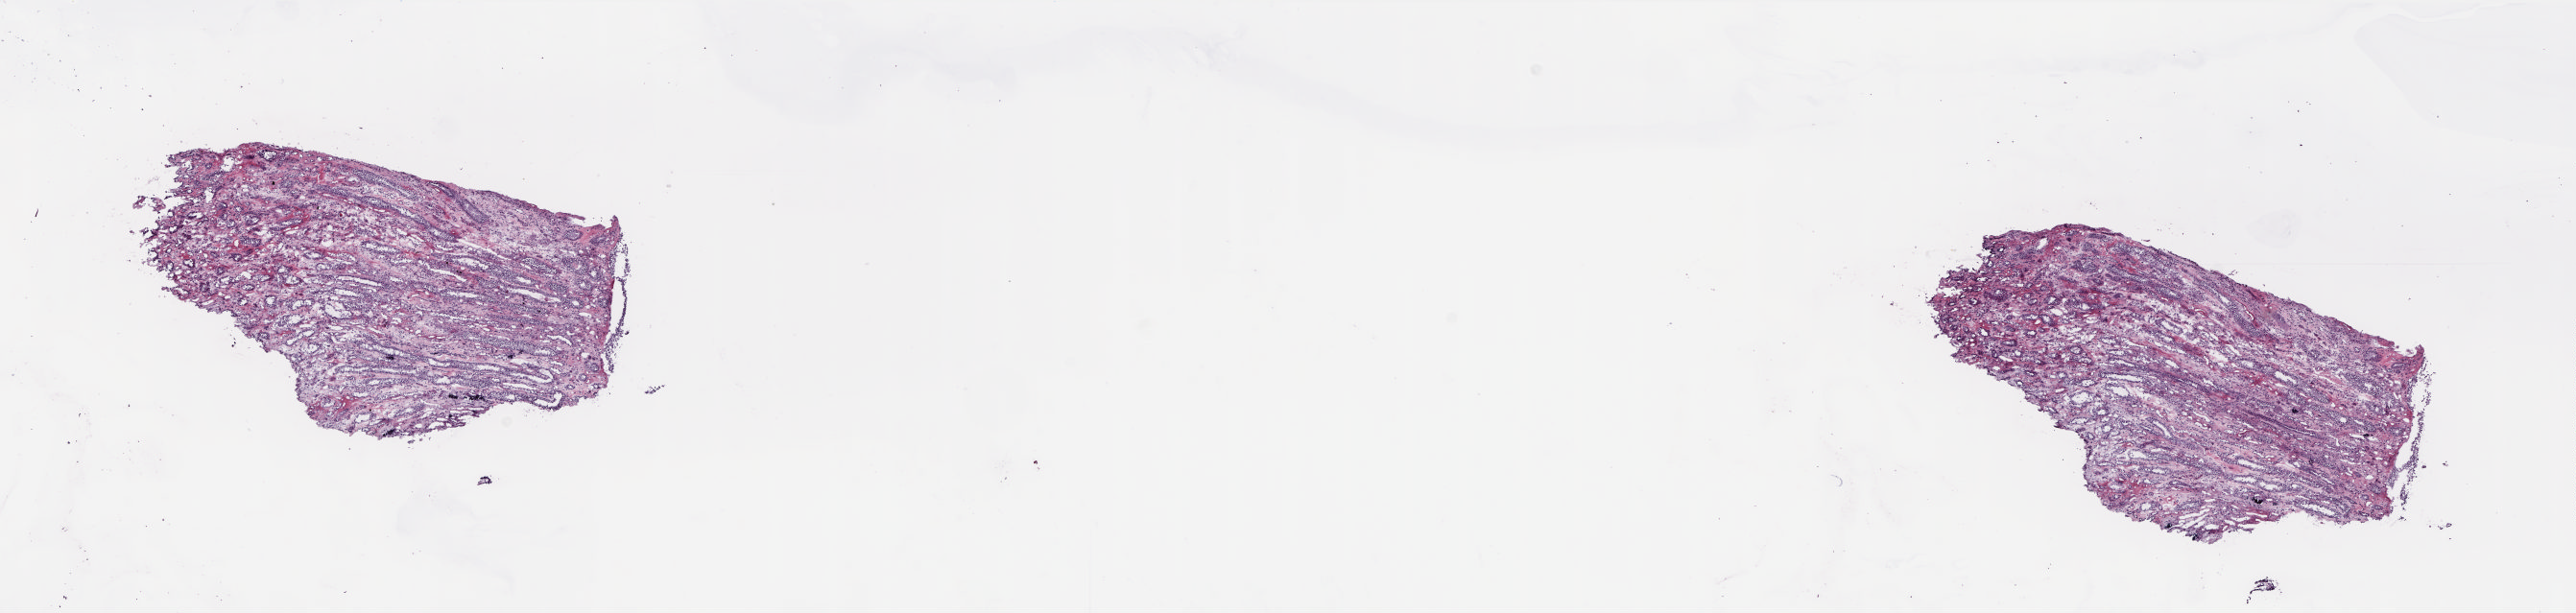
H&E whole-slide image, shown as a low-resolution overview of the whole scanned area (about 21.6 x 5.2 mm, slide scanned at 20x). Frozen section from the top of the tissue portion. Kidney, solid tissue normal (non-tumour tissue) sample. Male patient; age at initial diagnosis 61 years. Slide review estimates, as recorded: tumour cells 0%, tumour nuclei 0%, normal cells 100%, stromal cells 0%, necrosis 0%. Inflammatory infiltration, as recorded: lymphocyte infiltration 2%, monocyte infiltration 1%, neutrophil infiltration 0%.
• this section: solid tissue normal sample (biorepository sample class)
• patient diagnosis: Clear cell adenocarcinoma, NOS